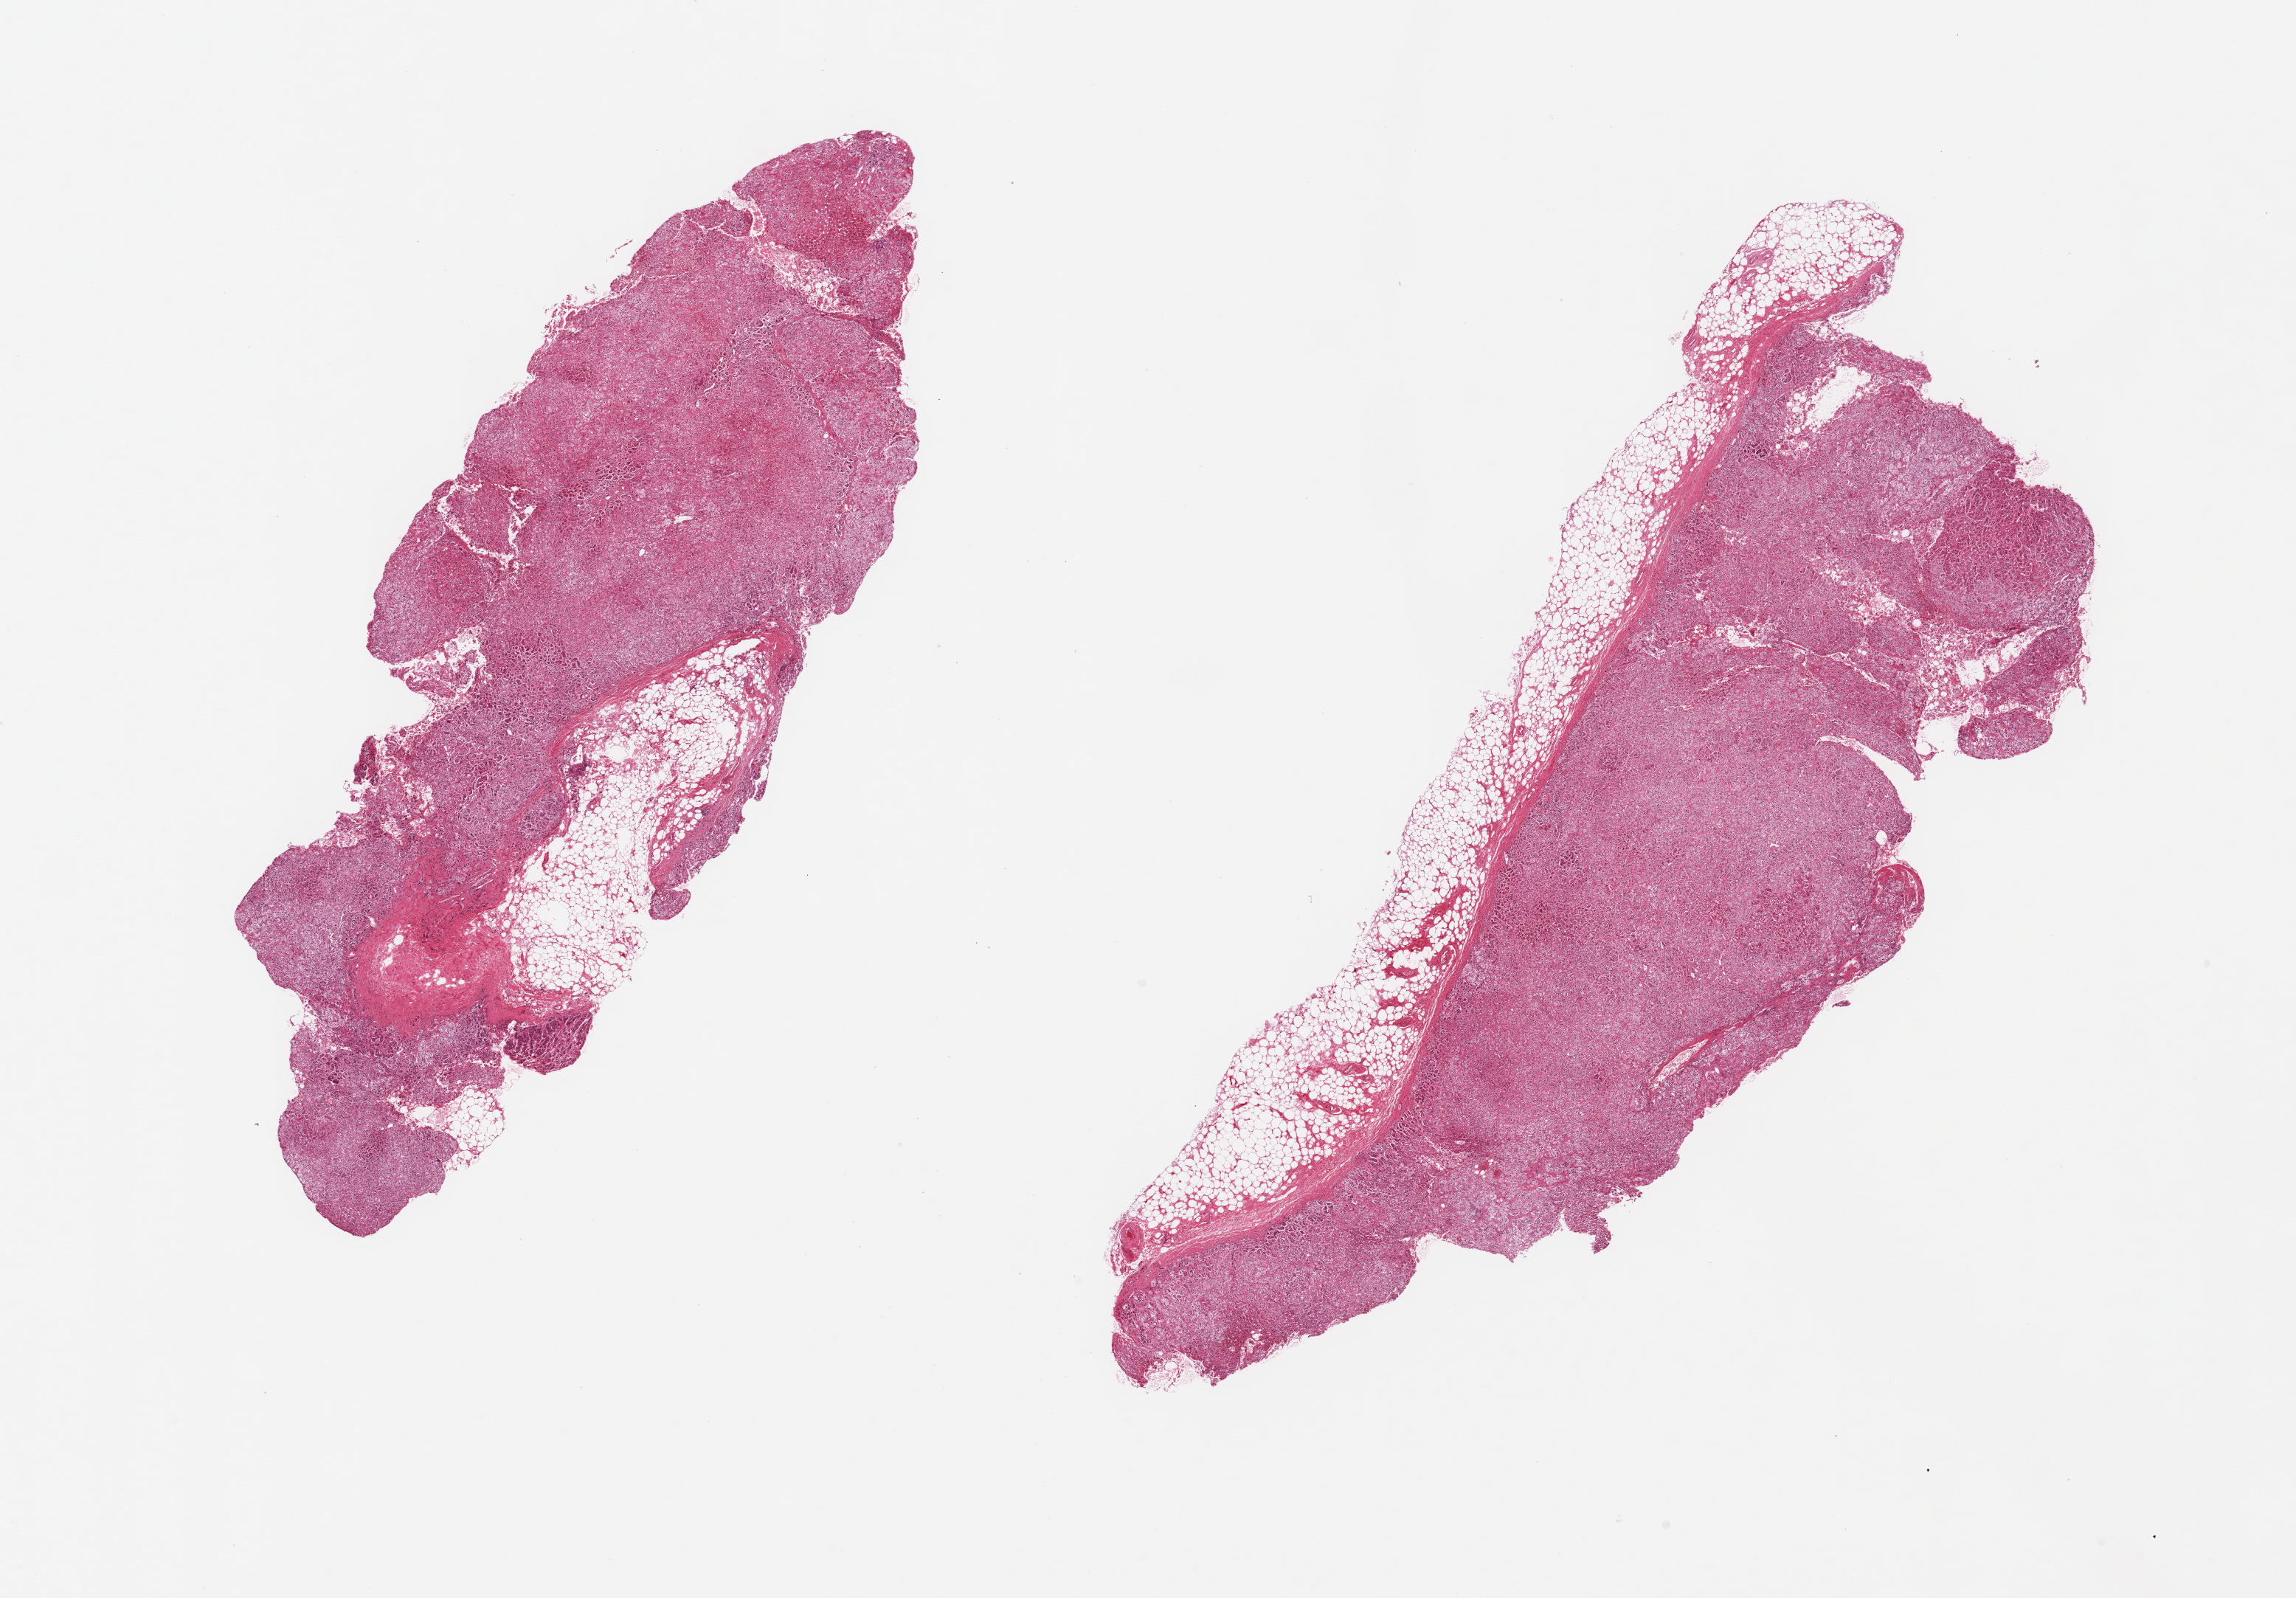
Hematoxylin and eosin (H&E) whole-slide image — a low-resolution overview of the entire scanned area, about 24.6 x 17.1 mm (acquisition: 20x scan), PAXgene-fixed paraffin-embedded (PFPE) section, target tissue: adrenal gland, tissue donor sample. Donor: male.
Reviewer comment on this tissue sample: 2 pieces, cortex, advanced autolysis; ~15-20% adherent fat.